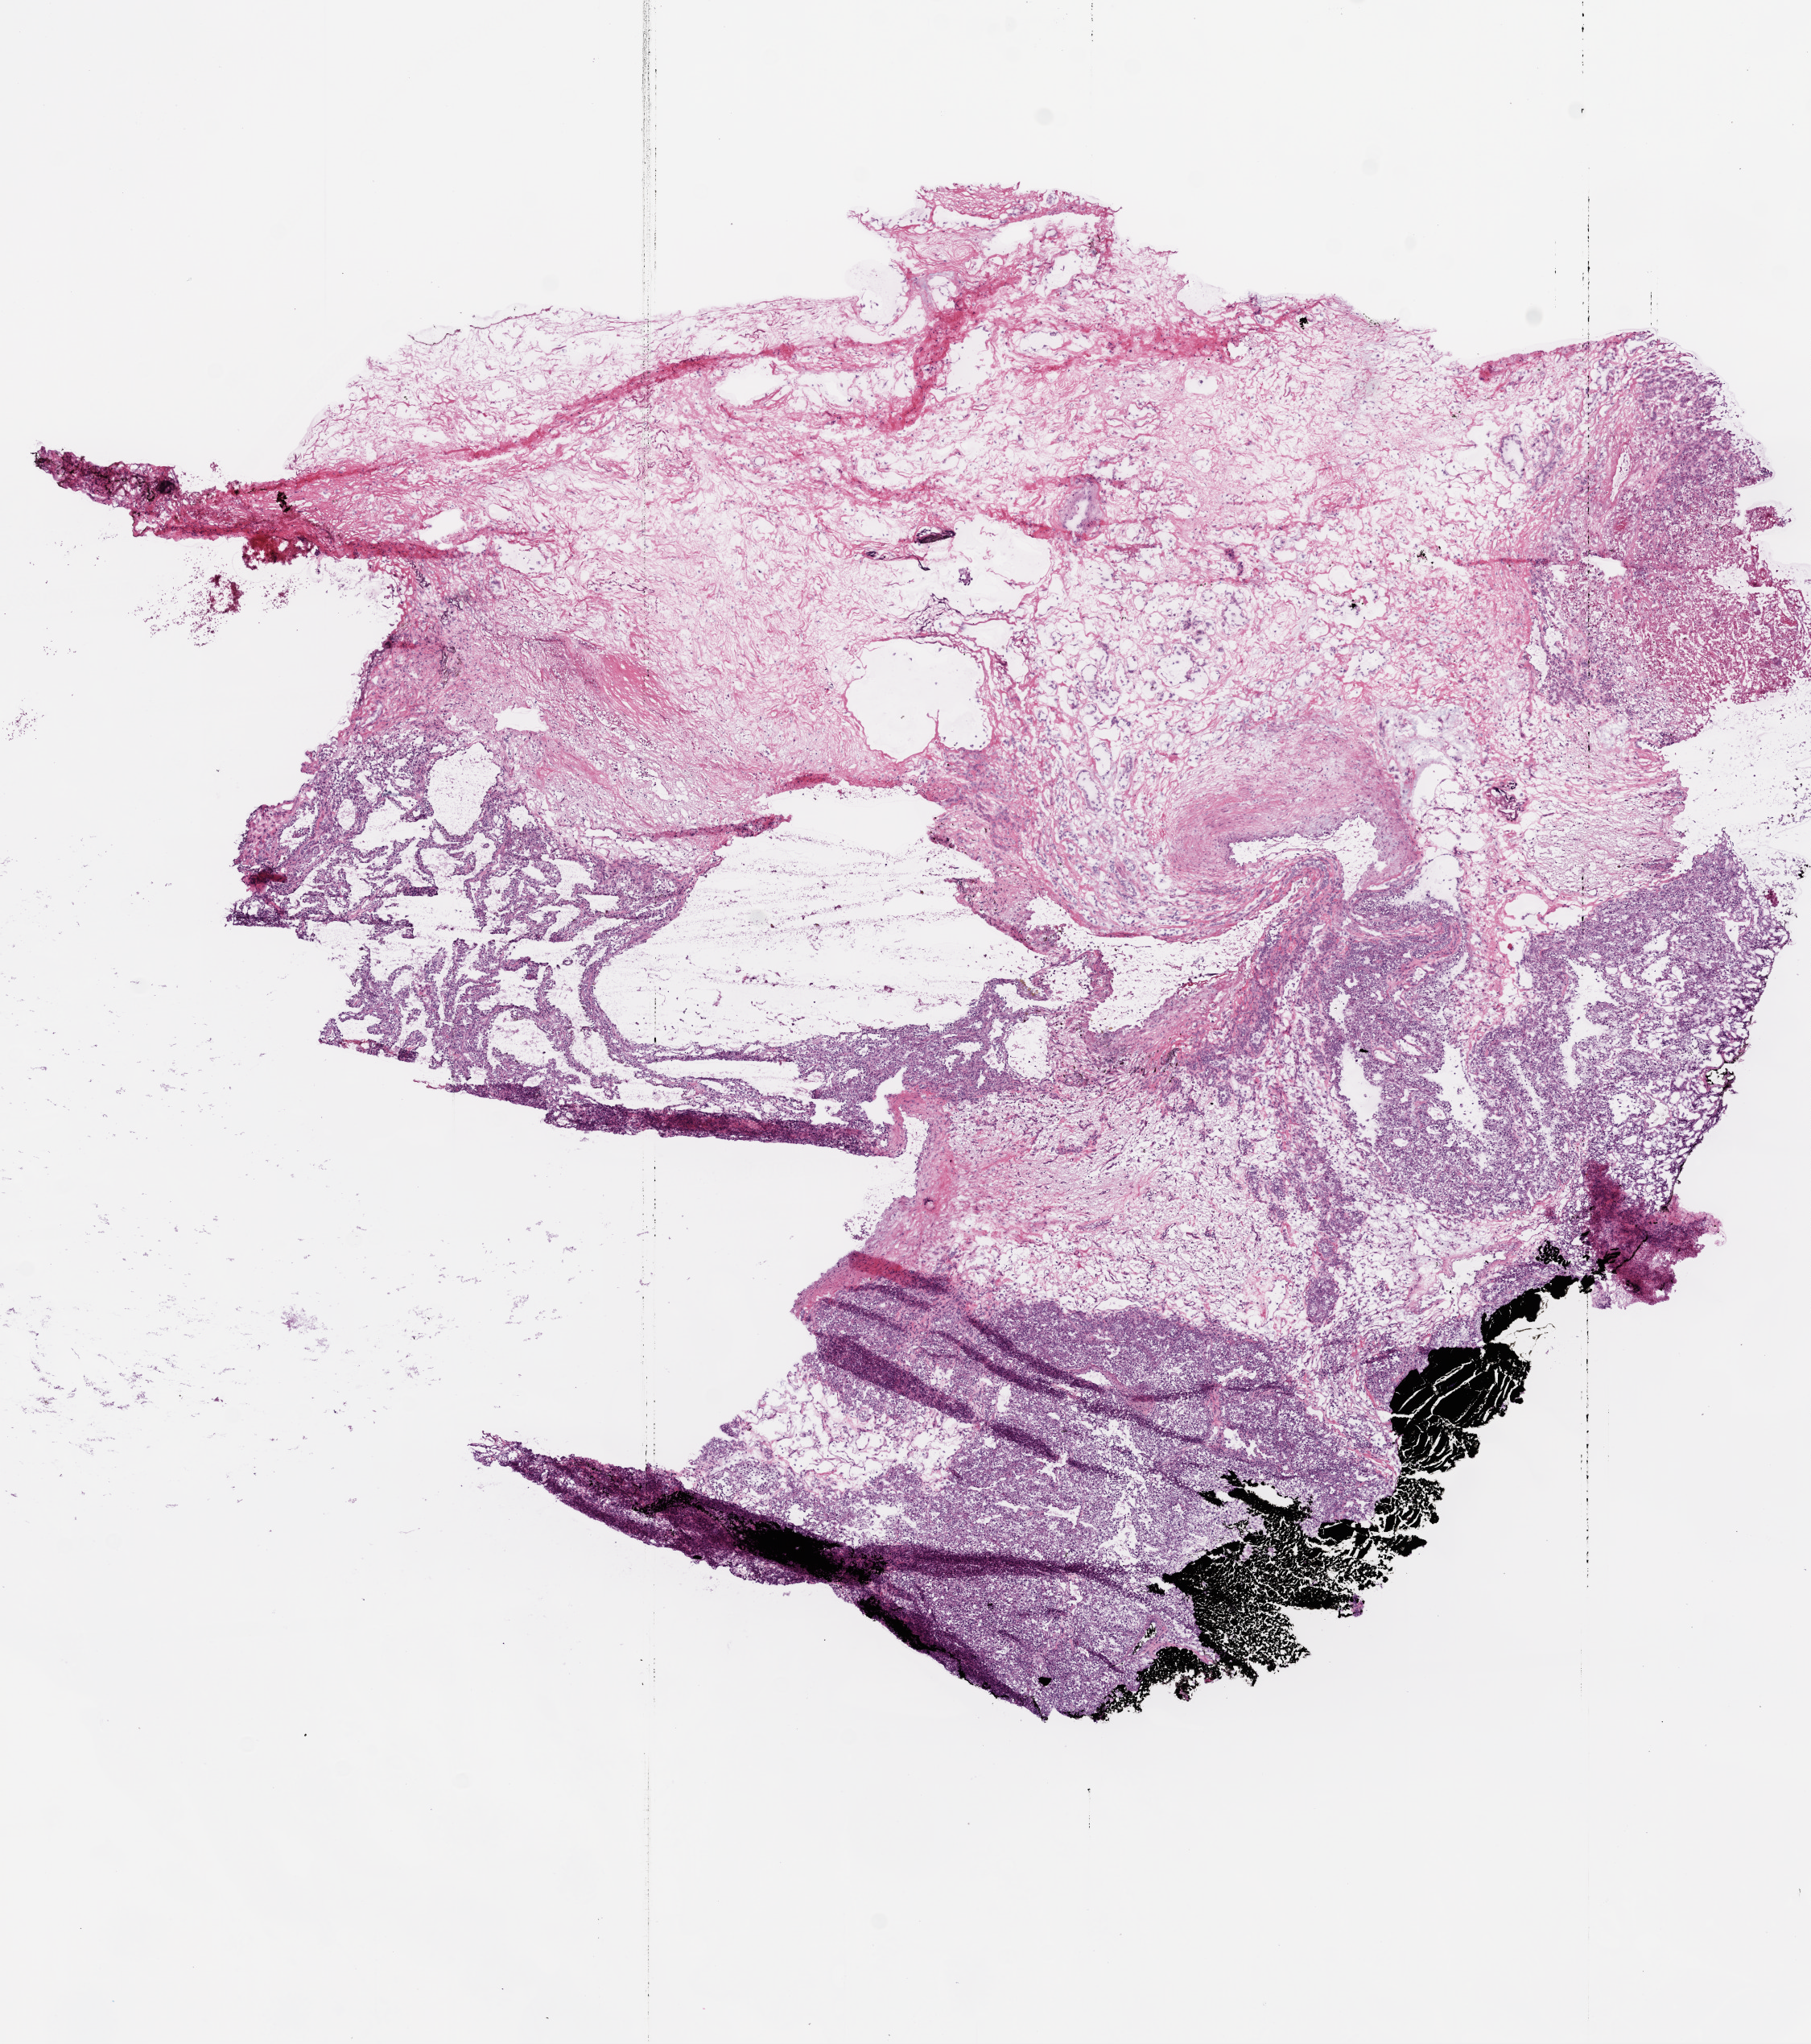
Whole-slide histology image, H&E — low-resolution overview of the scanned area, about 9.0 x 10.2 mm (from a 20x scan). Frozen section. Sample: primary tumour, kidney. Male patient; age at initial diagnosis 51 years. Histologic grade: G3 (poorly differentiated). Pathologist review of this section (percent, as recorded): tumour cells 30%, tumour nuclei 85%, normal cells 55%, stromal cells 5%, necrosis 10%.
AJCC pathologic stage: I. Histologic diagnosis: Clear cell adenocarcinoma, NOS. Laterality: right. TNM: T1b NX M0.